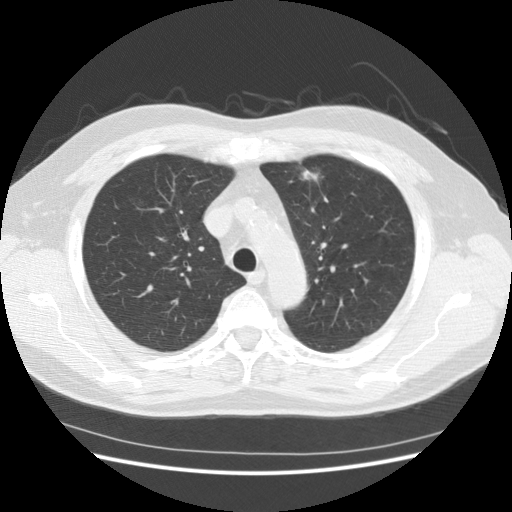
Axial slice from a low-dose chest CT screening exam. Baseline screening round. Lung window (W 1500 / L -600 HU). Standard (soft-tissue) reconstruction kernel (STANDARD). 512 × 512 image matrix, field of view 360 × 360 mm. Male, age 63 years at enrolment. Former smoker at enrolment.
• Lesion marked by an expert reader, bounding box [x1, y1, x2, y2] px = [281, 155, 337, 204].
• Reader record for this screening exam (exam-level; its link to the box is not recorded): non-calcified nodule or mass ≥4 mm, lingula, 18 × 9 mm, poorly defined margins, soft tissue attenuation.
• Lung cancer was diagnosed 475 days after this screen (after the second annual screen): adenocarcinoma, NOS, left upper lobe, moderately differentiated (G2), stage IA (AJCC 6th edition), 14 mm at pathology.